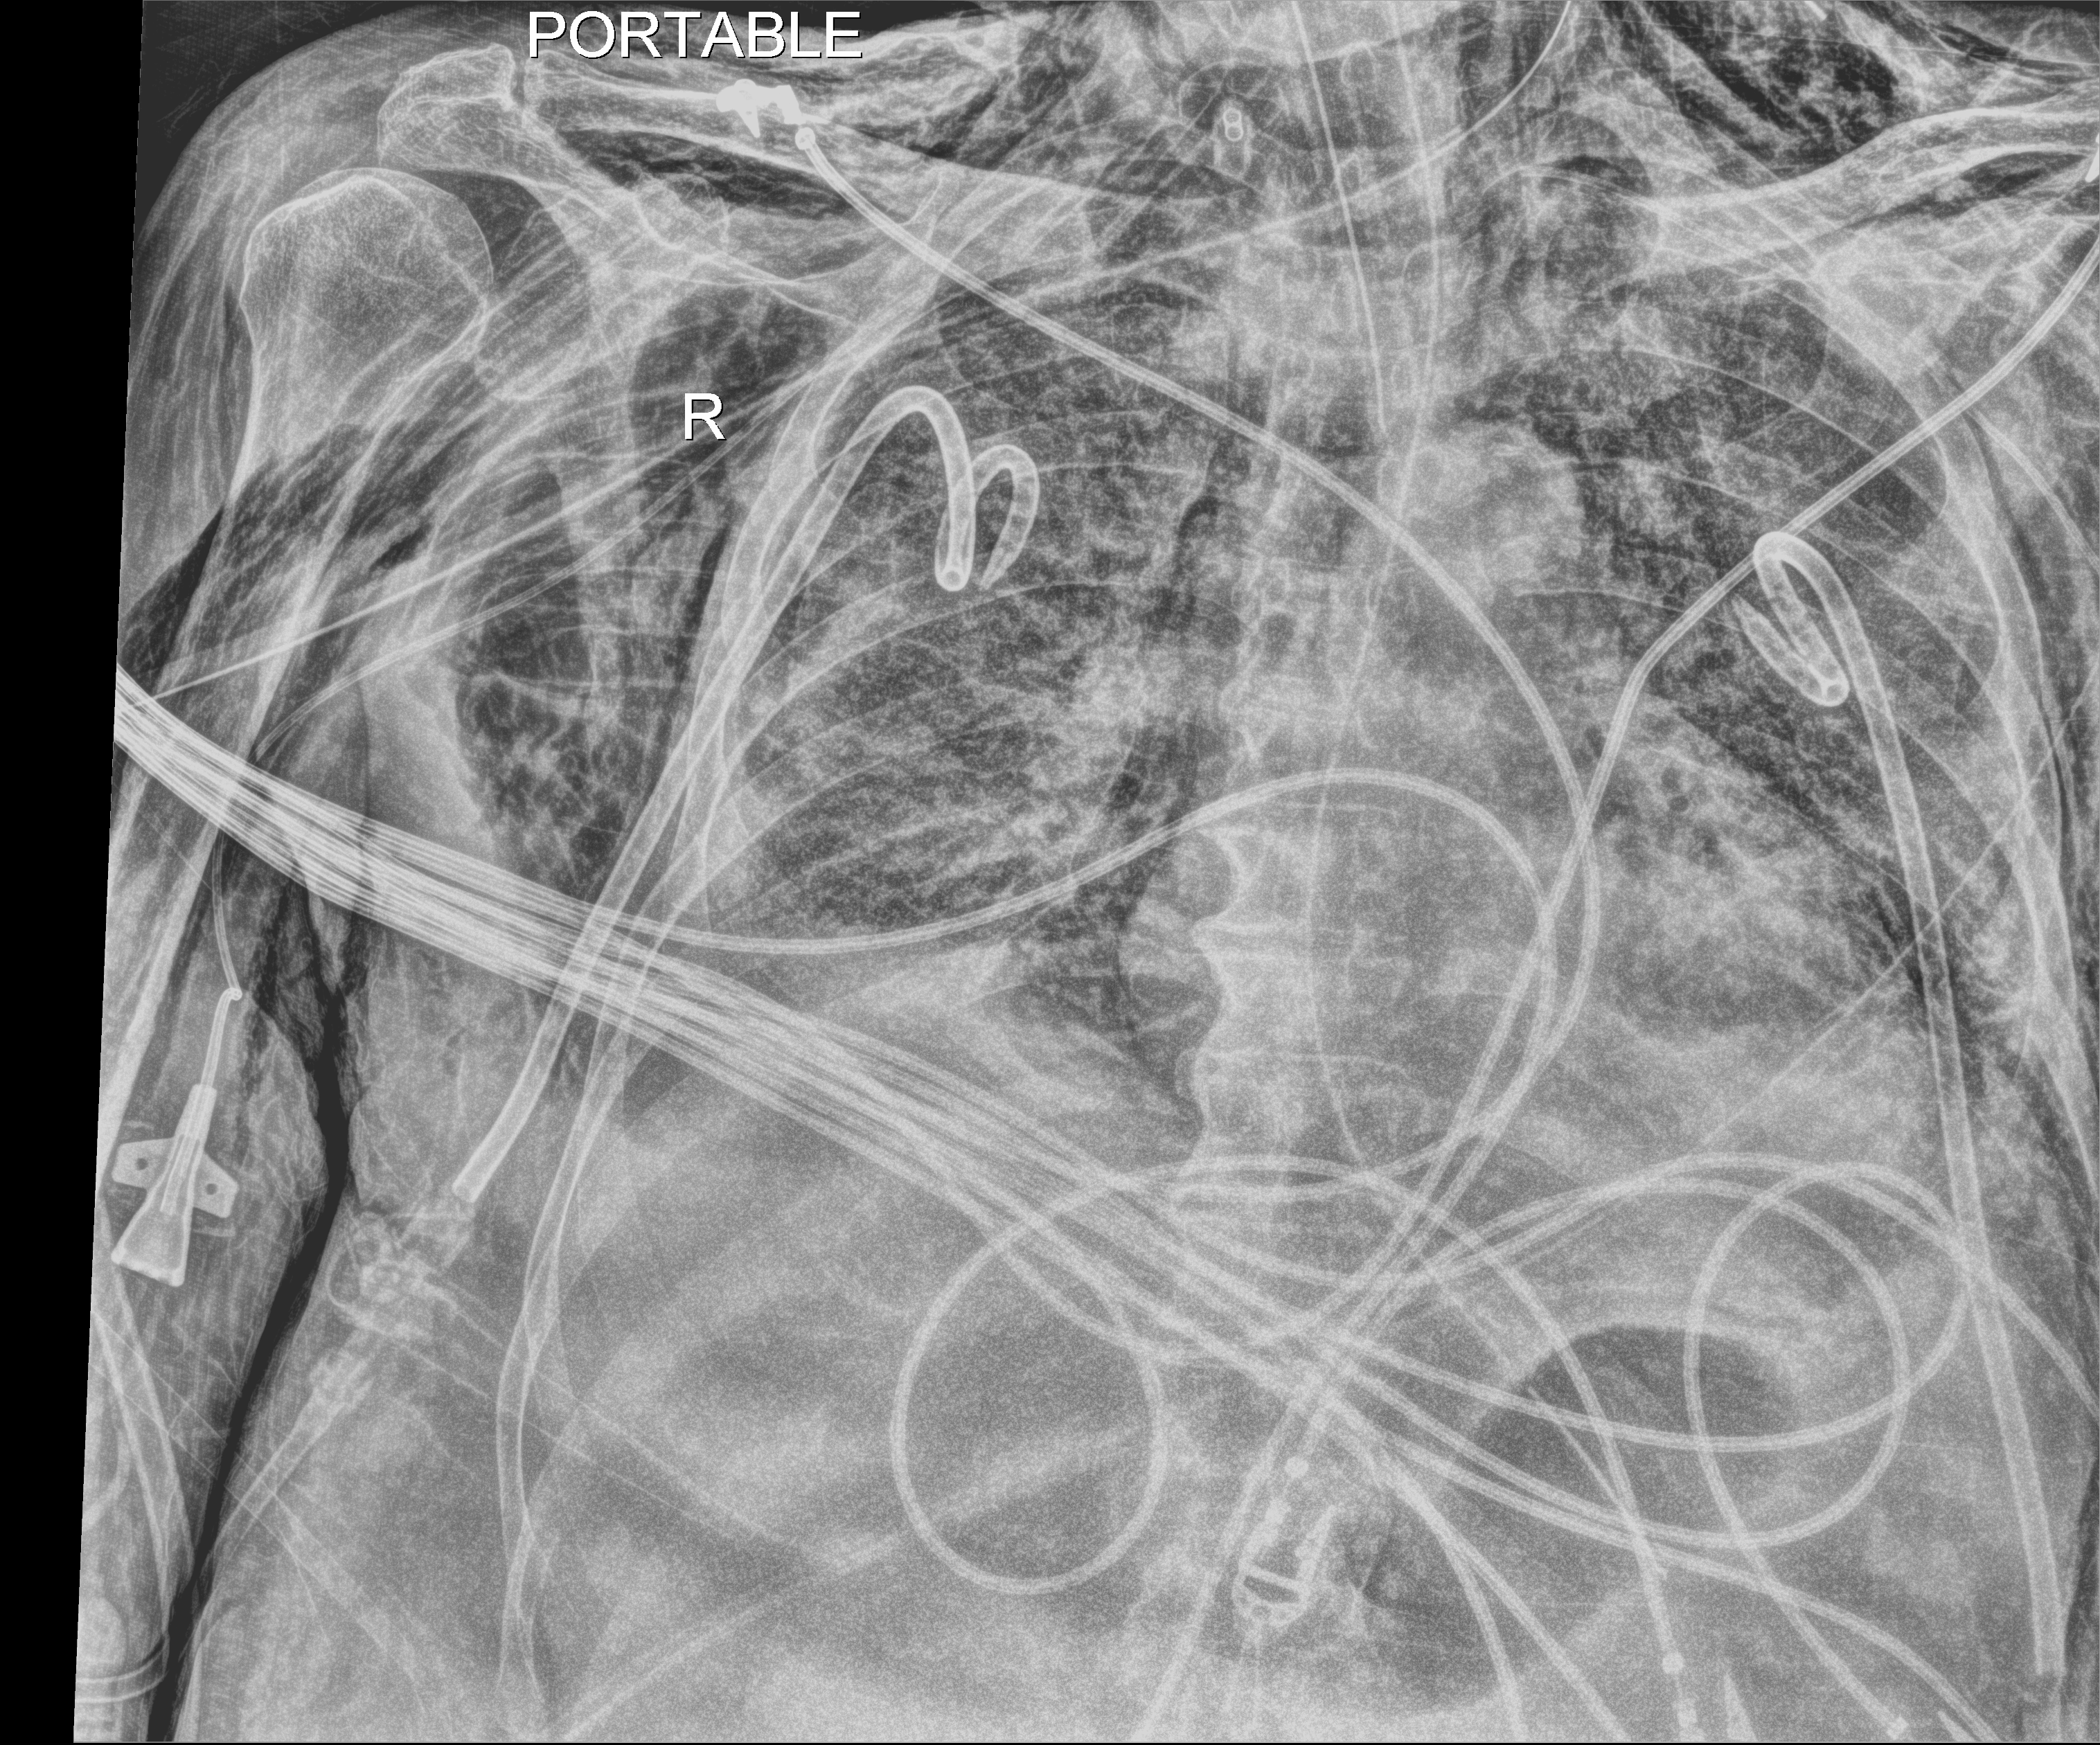
Portable chest radiograph; anteroposterior (AP) projection. Male patient hospitalised with COVID-19, age 75–90 years.
From the hospital-stay record, not from the radiograph (when in the stay this image was taken is not recorded): admitted to intensive care during this hospital stay: yes; COPD (admission record): no.